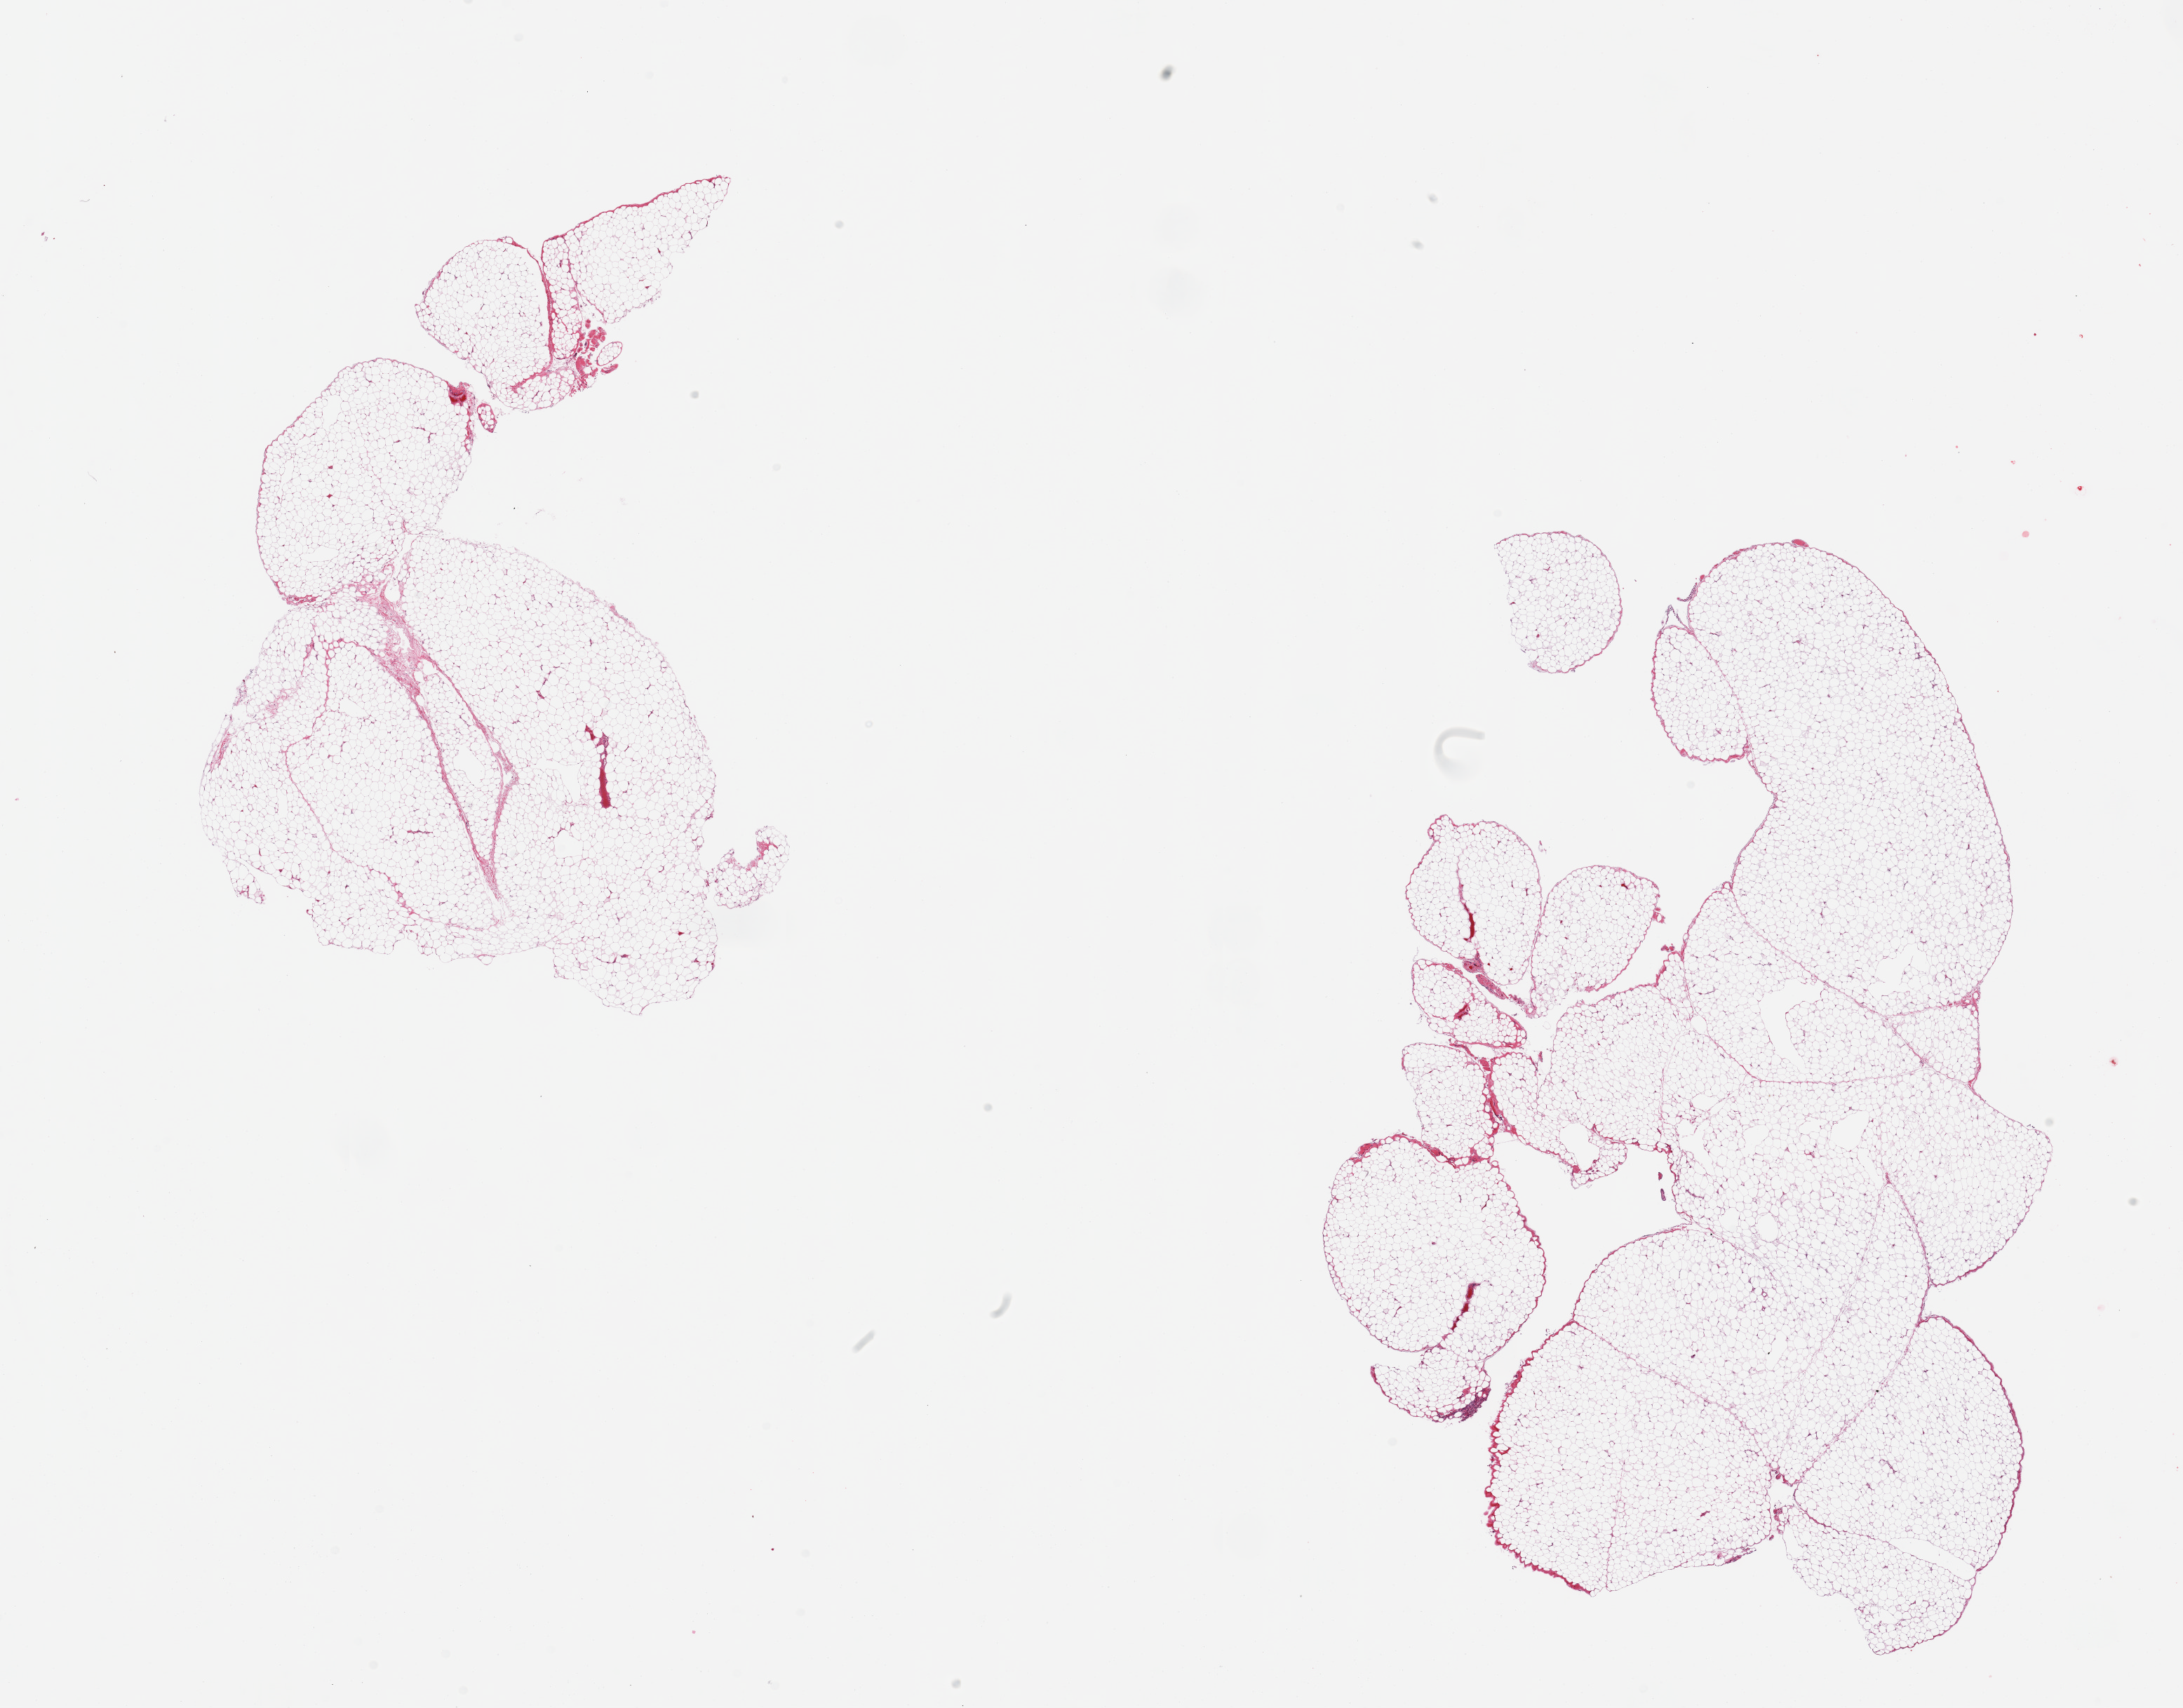
Digitized H&E-stained section, brightfield — a low-resolution overview of the entire scanned area, about 24.6 x 19.3 mm (acquisition: 20x scan); PAXgene-fixed paraffin-embedded (PFPE) section; section of omentum (target tissue); donor tissue sample. Female donor.
Pathologist's review note for this sample: 2 pieces; mature fat.